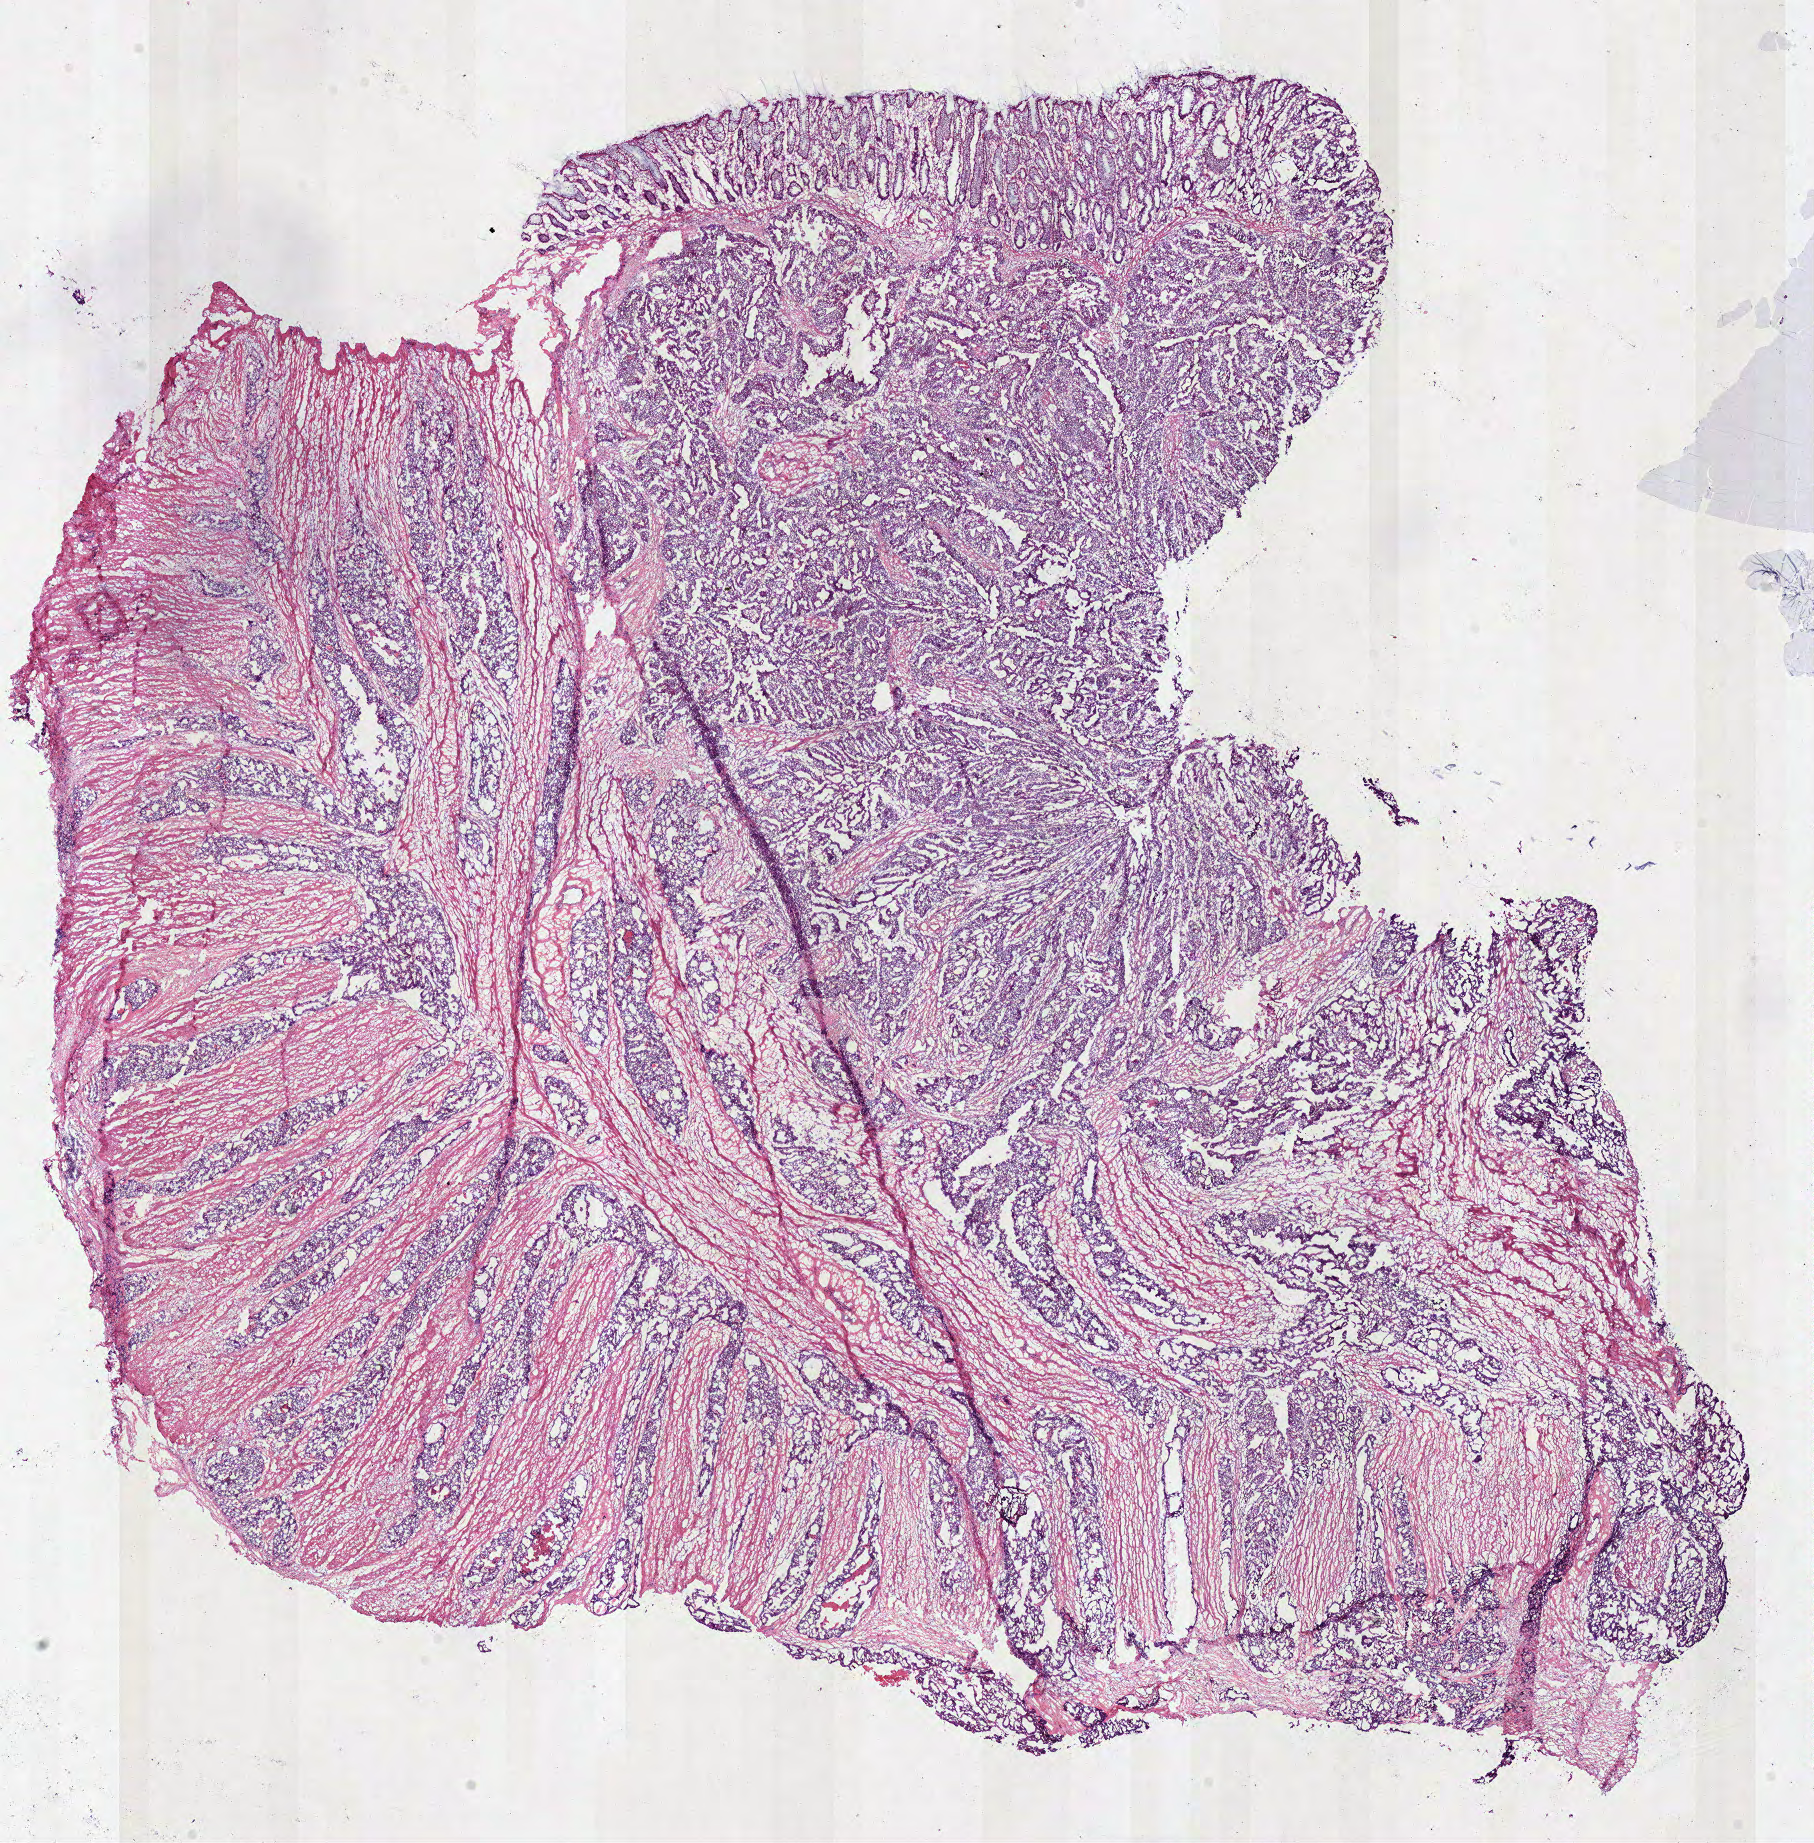
Whole-slide histology image, Hematoxylin and eosin (H&E) stained — low-resolution overview of the scanned area, about 14.3 x 14.5 mm (slide scanned at 40x). Frozen section from the top of the tissue portion. Primary tumour sample from the rectum. Female, age 71 years at initial diagnosis. Pathologist review of this section (percent, as recorded): tumour cells 81%, tumour nuclei 80%, normal cells 2%, stromal cells 15%, necrosis 2%.
AJCC pathologic stage: IIIB. Pathologic diagnosis: Adenocarcinoma, NOS. Lymph nodes positive (case pathology): 3 of 6 examined.